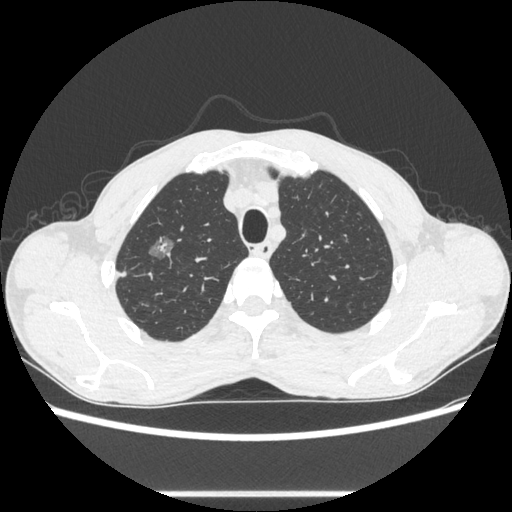
Chest CT, one axial slice. Slice 489 of 600 in the series (ordered by position). Reconstruction kernel STANDARD. 100 kVp. Lung window (W 1500 / L -600 HU). 0.62 mm slice thickness. 512 × 512 image matrix, field of view 357 × 357 mm. Patient: male, 54 years. From the clinical record (not read from this slice): clinical TNM (as recorded): T1a N0 M0.
Structures marked on this image (rectangle marked by the reading radiologist):
- lung tumour (recorded histology: adenocarcinoma): bounding box [x1, y1, x2, y2] px = [142, 227, 173, 259]